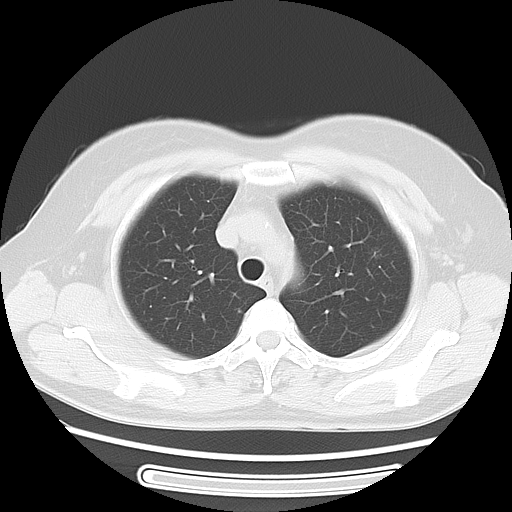
Chest CT, one axial slice. Slice 39 of 52 in the series (ordered by position). Lung window (W 1500 / L -600 HU). 5 mm slice thickness. 512 × 512 image matrix, field of view 350 × 350 mm. Patient: female, 54 years. From the clinical record (not read from this slice): clinical TNM (as recorded): T1c N0 M0.
Outlined on this slice (bounding box drawn by a radiologist):
- lung tumour (recorded histology: adenocarcinoma): bounding box (x1, y1, x2, y2) in pixels: (363, 241, 389, 267)